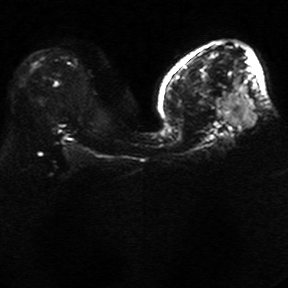
Breast MRI, one axial slice; slice 14 of 34 in the series (ordered by position); diffusion-weighted series; image 2 of 4 stored at this slice position (different b-values; order by instance number); 1.5 T; 5 mm slice thickness; 288 × 288 image matrix, field of view 340 × 340 mm. Female patient.
Annotated regions visible in this slice (manually delineated by an expert):
- tumour on diffusion-weighted imaging: bounding box (x1, y1, x2, y2) in pixels: (215, 93, 256, 127)